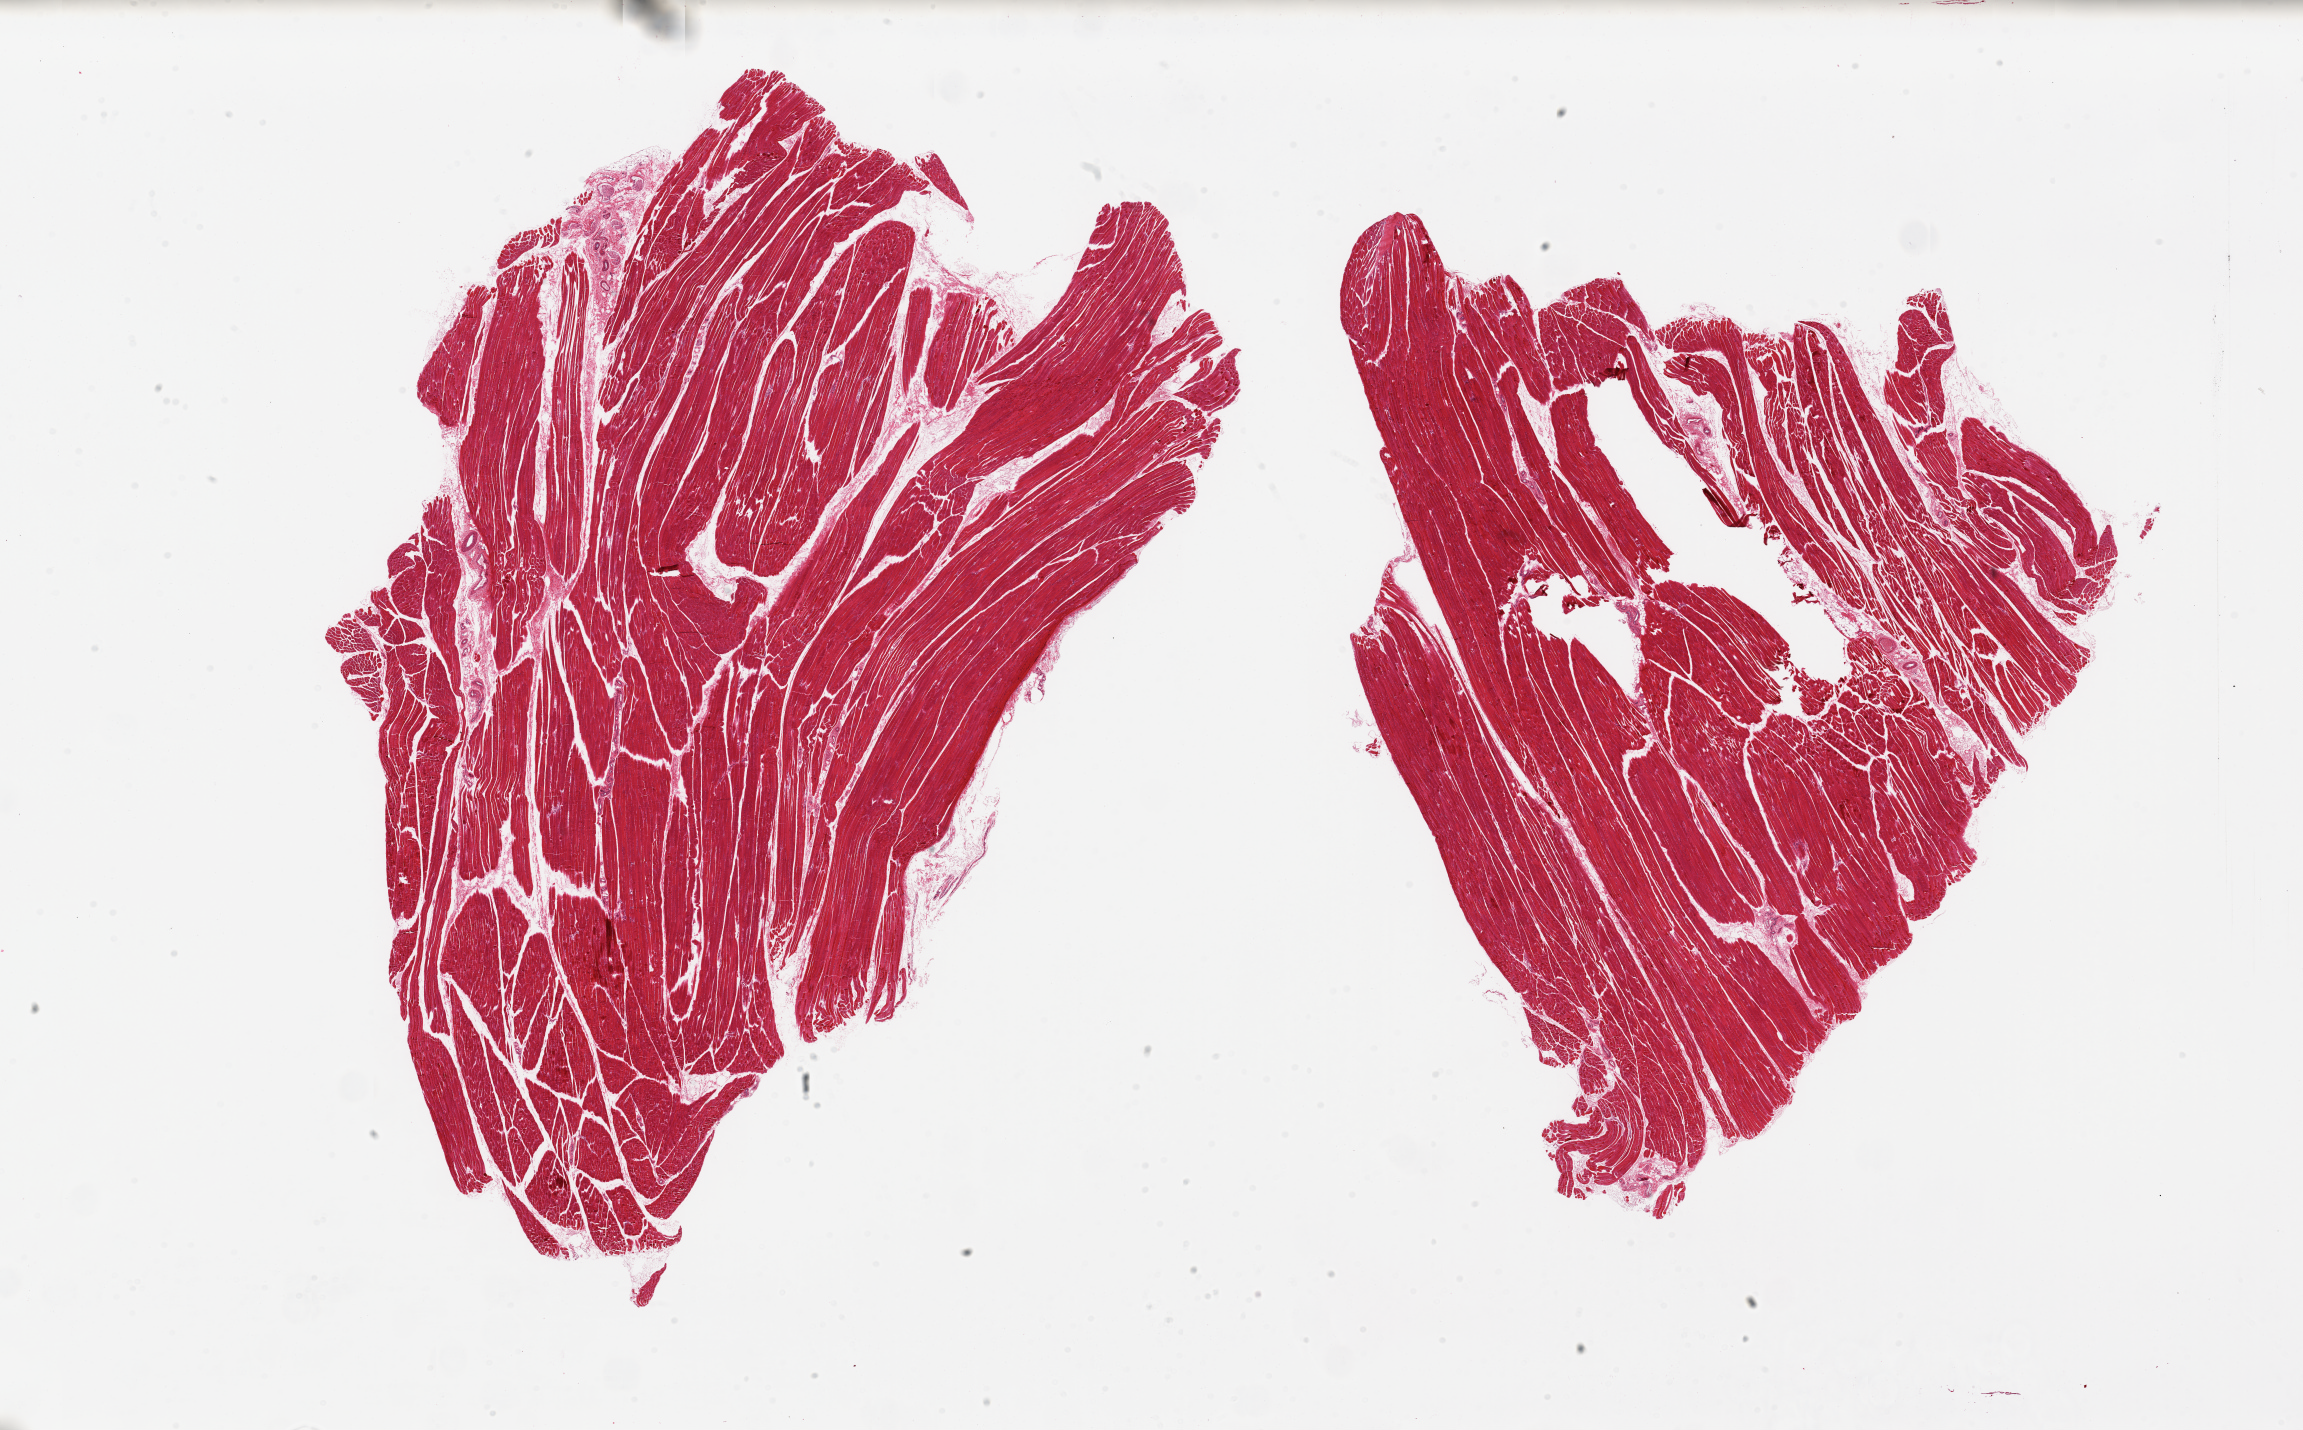
Whole-slide image, haematoxylin and eosin stain, low-resolution overview of the scanned area, about 36.4 x 22.6 mm (acquisition: 20x scan). Donor sex: female.
Specimen: PAXgene-fixed, paraffin-embedded tissue; target tissue: skeletal muscle; donor tissue sample.